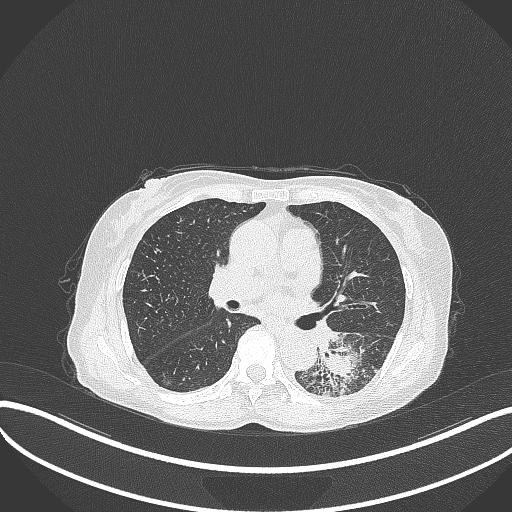
Chest CT, one axial slice. Position 174 of 370 along the scan axis. Reconstruction kernel B70f. Lung window (W 1500 / L -600 HU). 1 mm slice thickness. 512 × 512 image matrix. Female patient, age 78 years. Case-level facts recorded for this patient, not image findings: clinical TNM (as recorded): T3 N0 M1.
Annotated regions visible in this slice (rectangle marked by the reading radiologist):
- lung tumour (recorded histology: squamous cell carcinoma): bounding box [x1, y1, x2, y2] px = [312, 327, 379, 403]